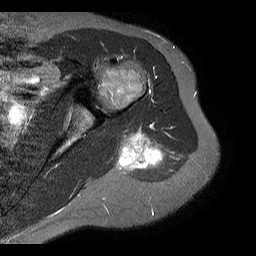
MRI of an extremity soft-tissue mass, one axial slice; slice 11 of 20 in the series (ordered by position); STIR; 256 × 256 image matrix, field of view 150 × 150 mm. Female patient. From the clinical record (not read from this slice): histological type: malignant fibrous histiocytoma; grade: low; site of the primary tumour: left arm.
Annotated regions visible in this slice (manually delineated by an expert):
- gross tumour volume (mass): bounding box [x1, y1, x2, y2] px = [116, 125, 165, 171]